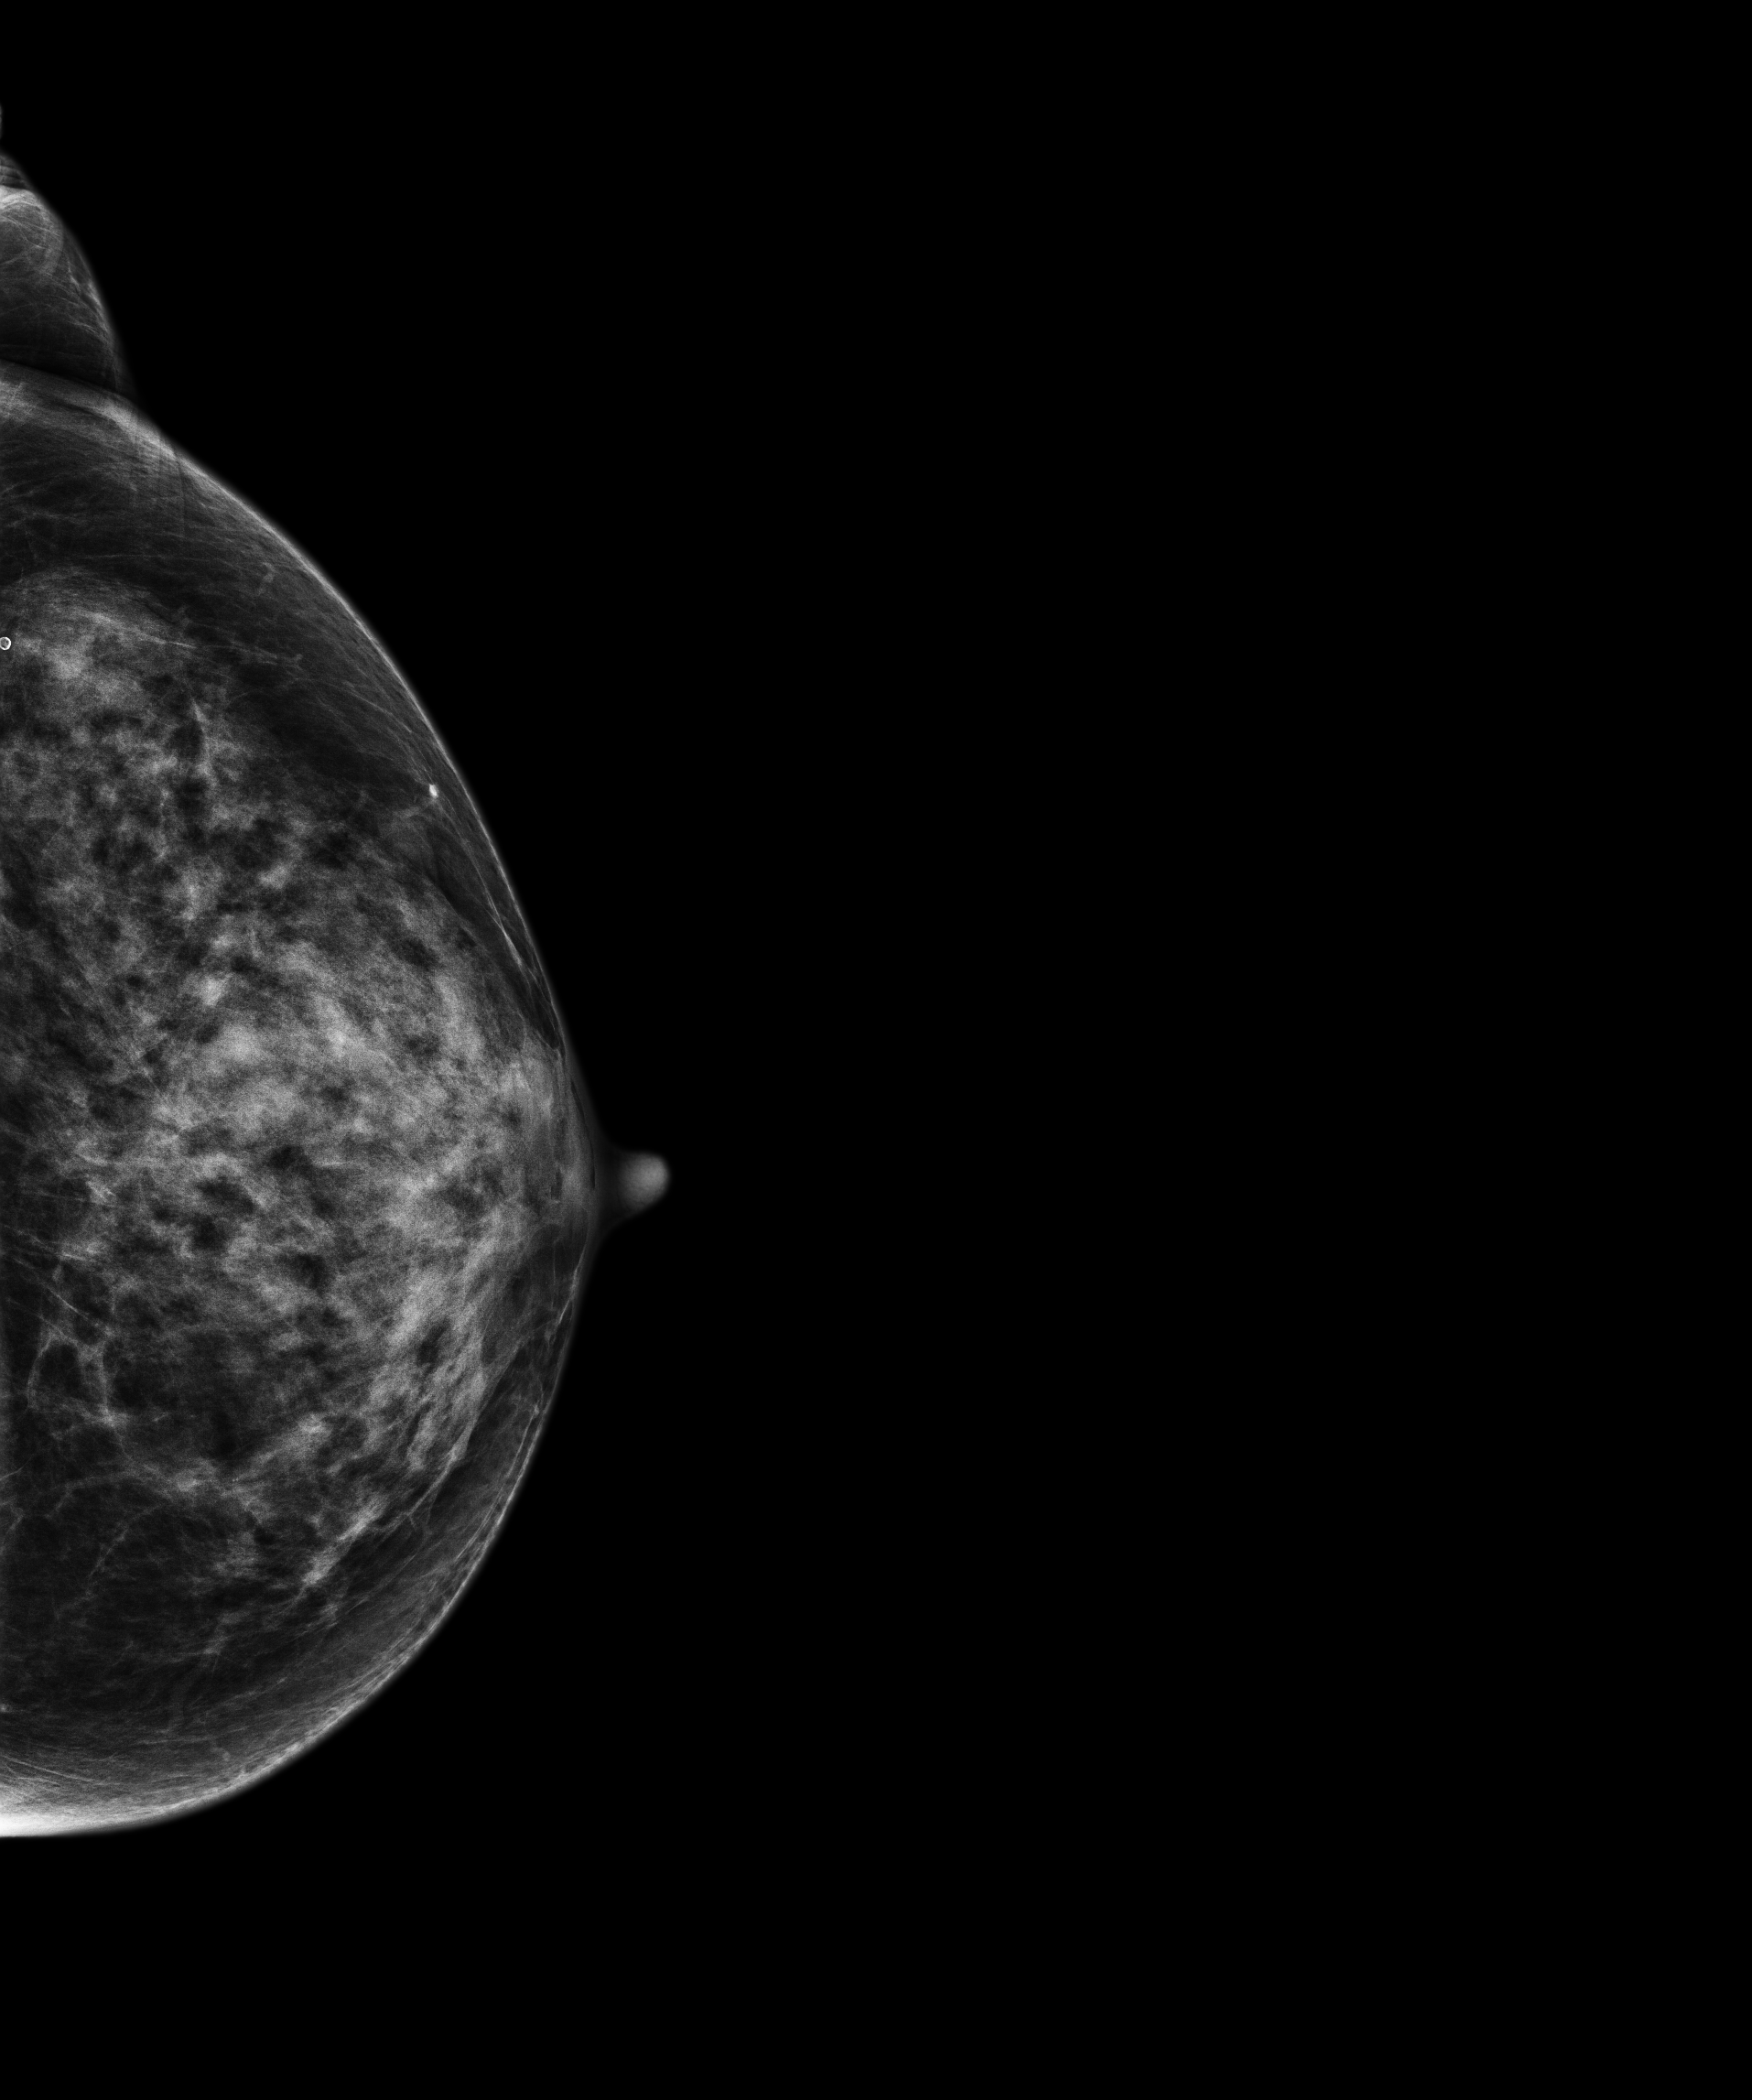
Annual screening mammography examination, compressed breast thickness 41.3 mm, system: Senographe Pristina. Female patient, age 68 years.
Image type: full-field digital mammogram. Breast: left. Projection: craniocaudal (CC) view.